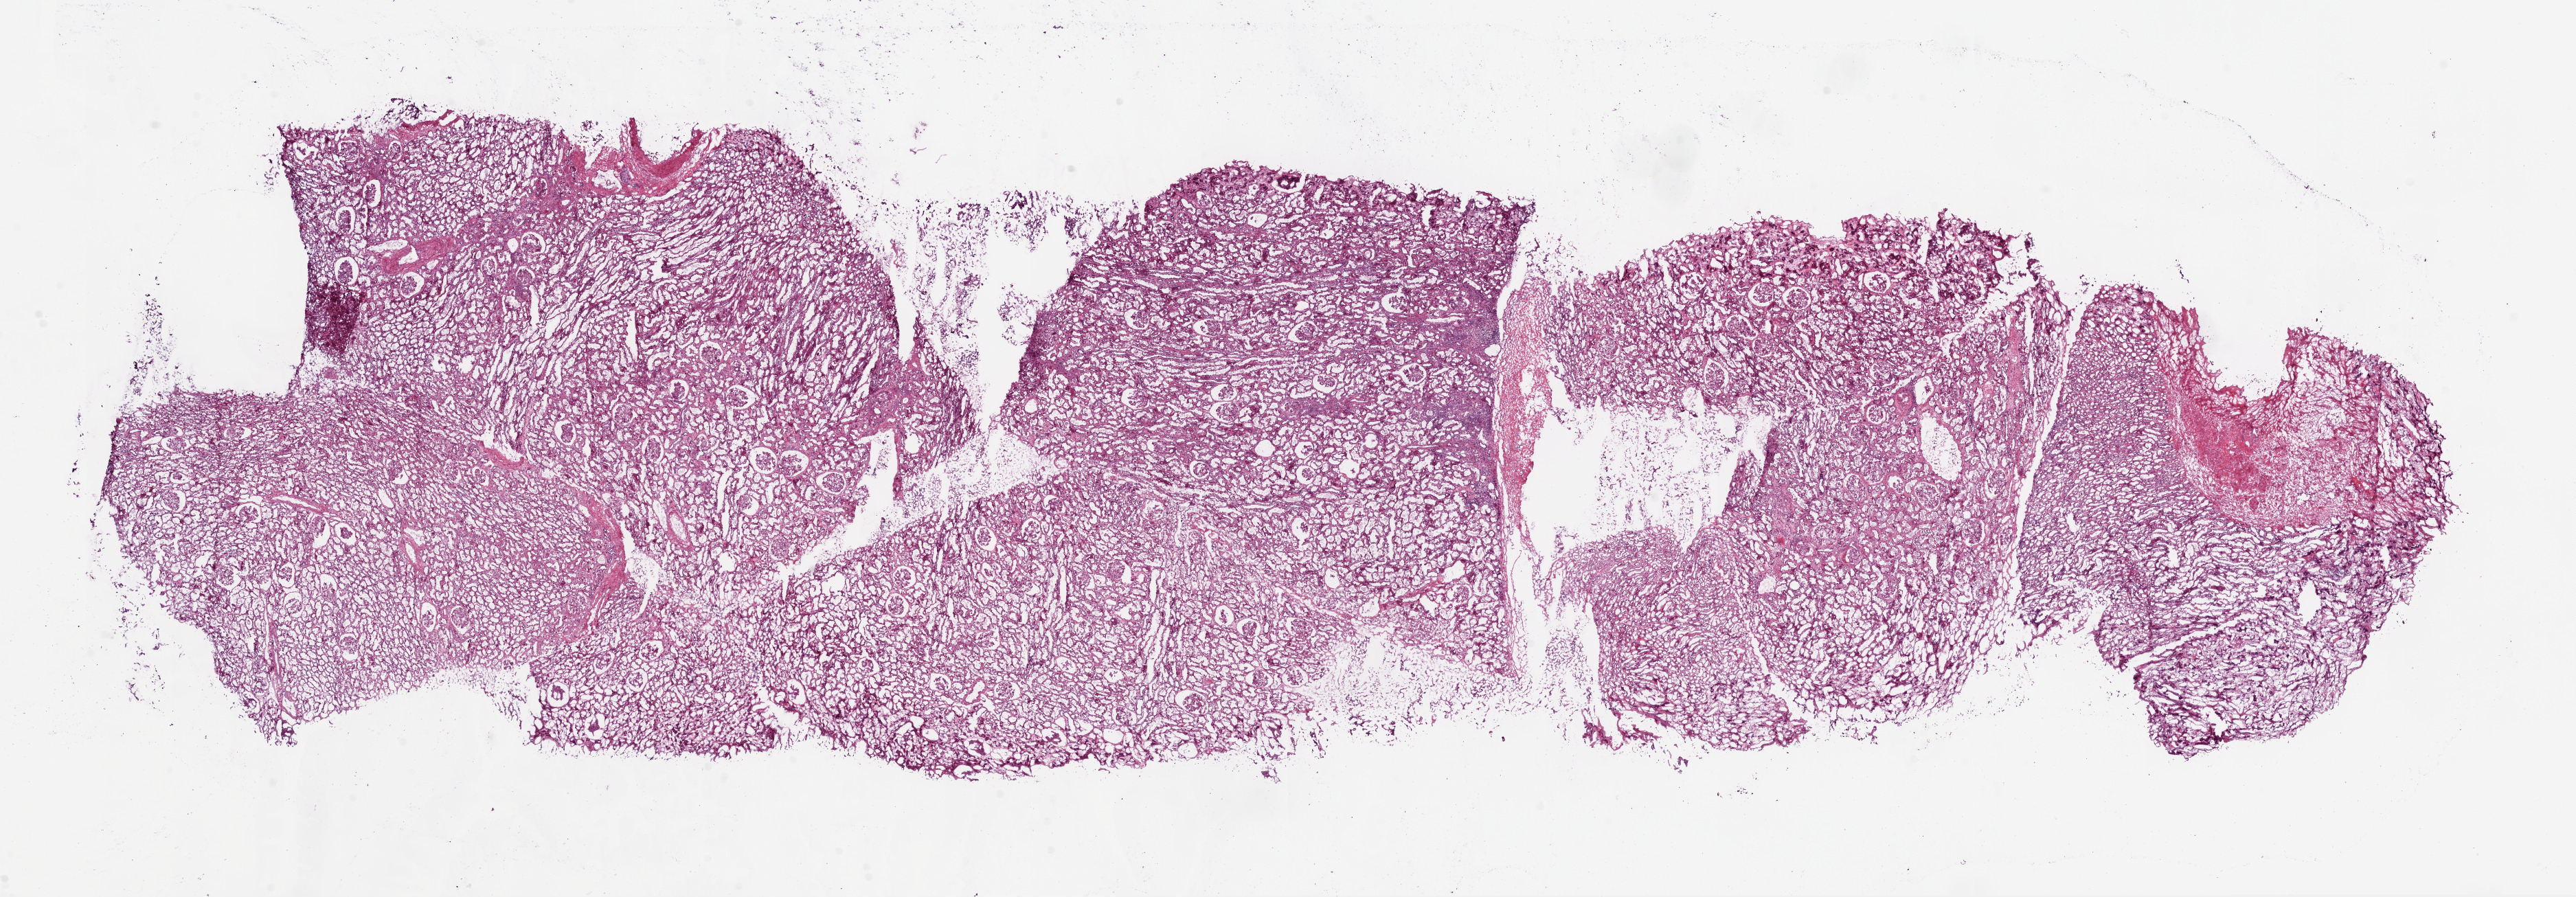
Digitized H&E tissue section (whole slide), whole scanned area (about 30.1 x 10.5 mm) shown as a low-resolution overview. Frozen section from the bottom of the tissue portion. Kidney, solid tissue normal (non-tumour tissue) sample. Male patient; age at initial diagnosis 49 years.
This section: solid tissue normal (non-tumour) sample from the same patient. Patient diagnosis: Clear cell adenocarcinoma, NOS.